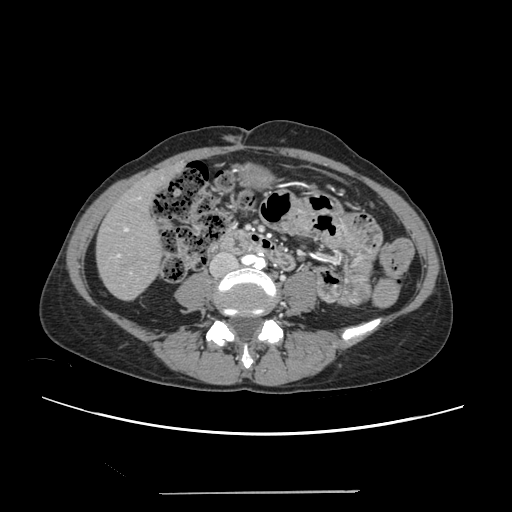
Contrast-enhanced abdominal CT, one axial slice. Slice 51 of 240 in the series (ordered by position). 120 kVp. Soft-tissue window (W 400 / L 40 HU). 1.25 mm slice thickness. 512 × 512 image matrix, field of view 371 × 371 mm. Female patient, age 60 years. From the clinical record (not read from this slice): diagnosis: colorectal cancer liver metastases, imaged before liver resection; multiple liver metastases: no; largest metastasis: 1.5 cm; disease in both lobes: no.
Structures marked on this image (expert manual segmentation):
- liver: bounding box [x1, y1, x2, y2] px = [97, 168, 176, 299]
- planned liver remnant (the part of the liver to remain after resection): [97, 171, 170, 299]
- portal vein (with intrahepatic branches): [113, 196, 141, 274]